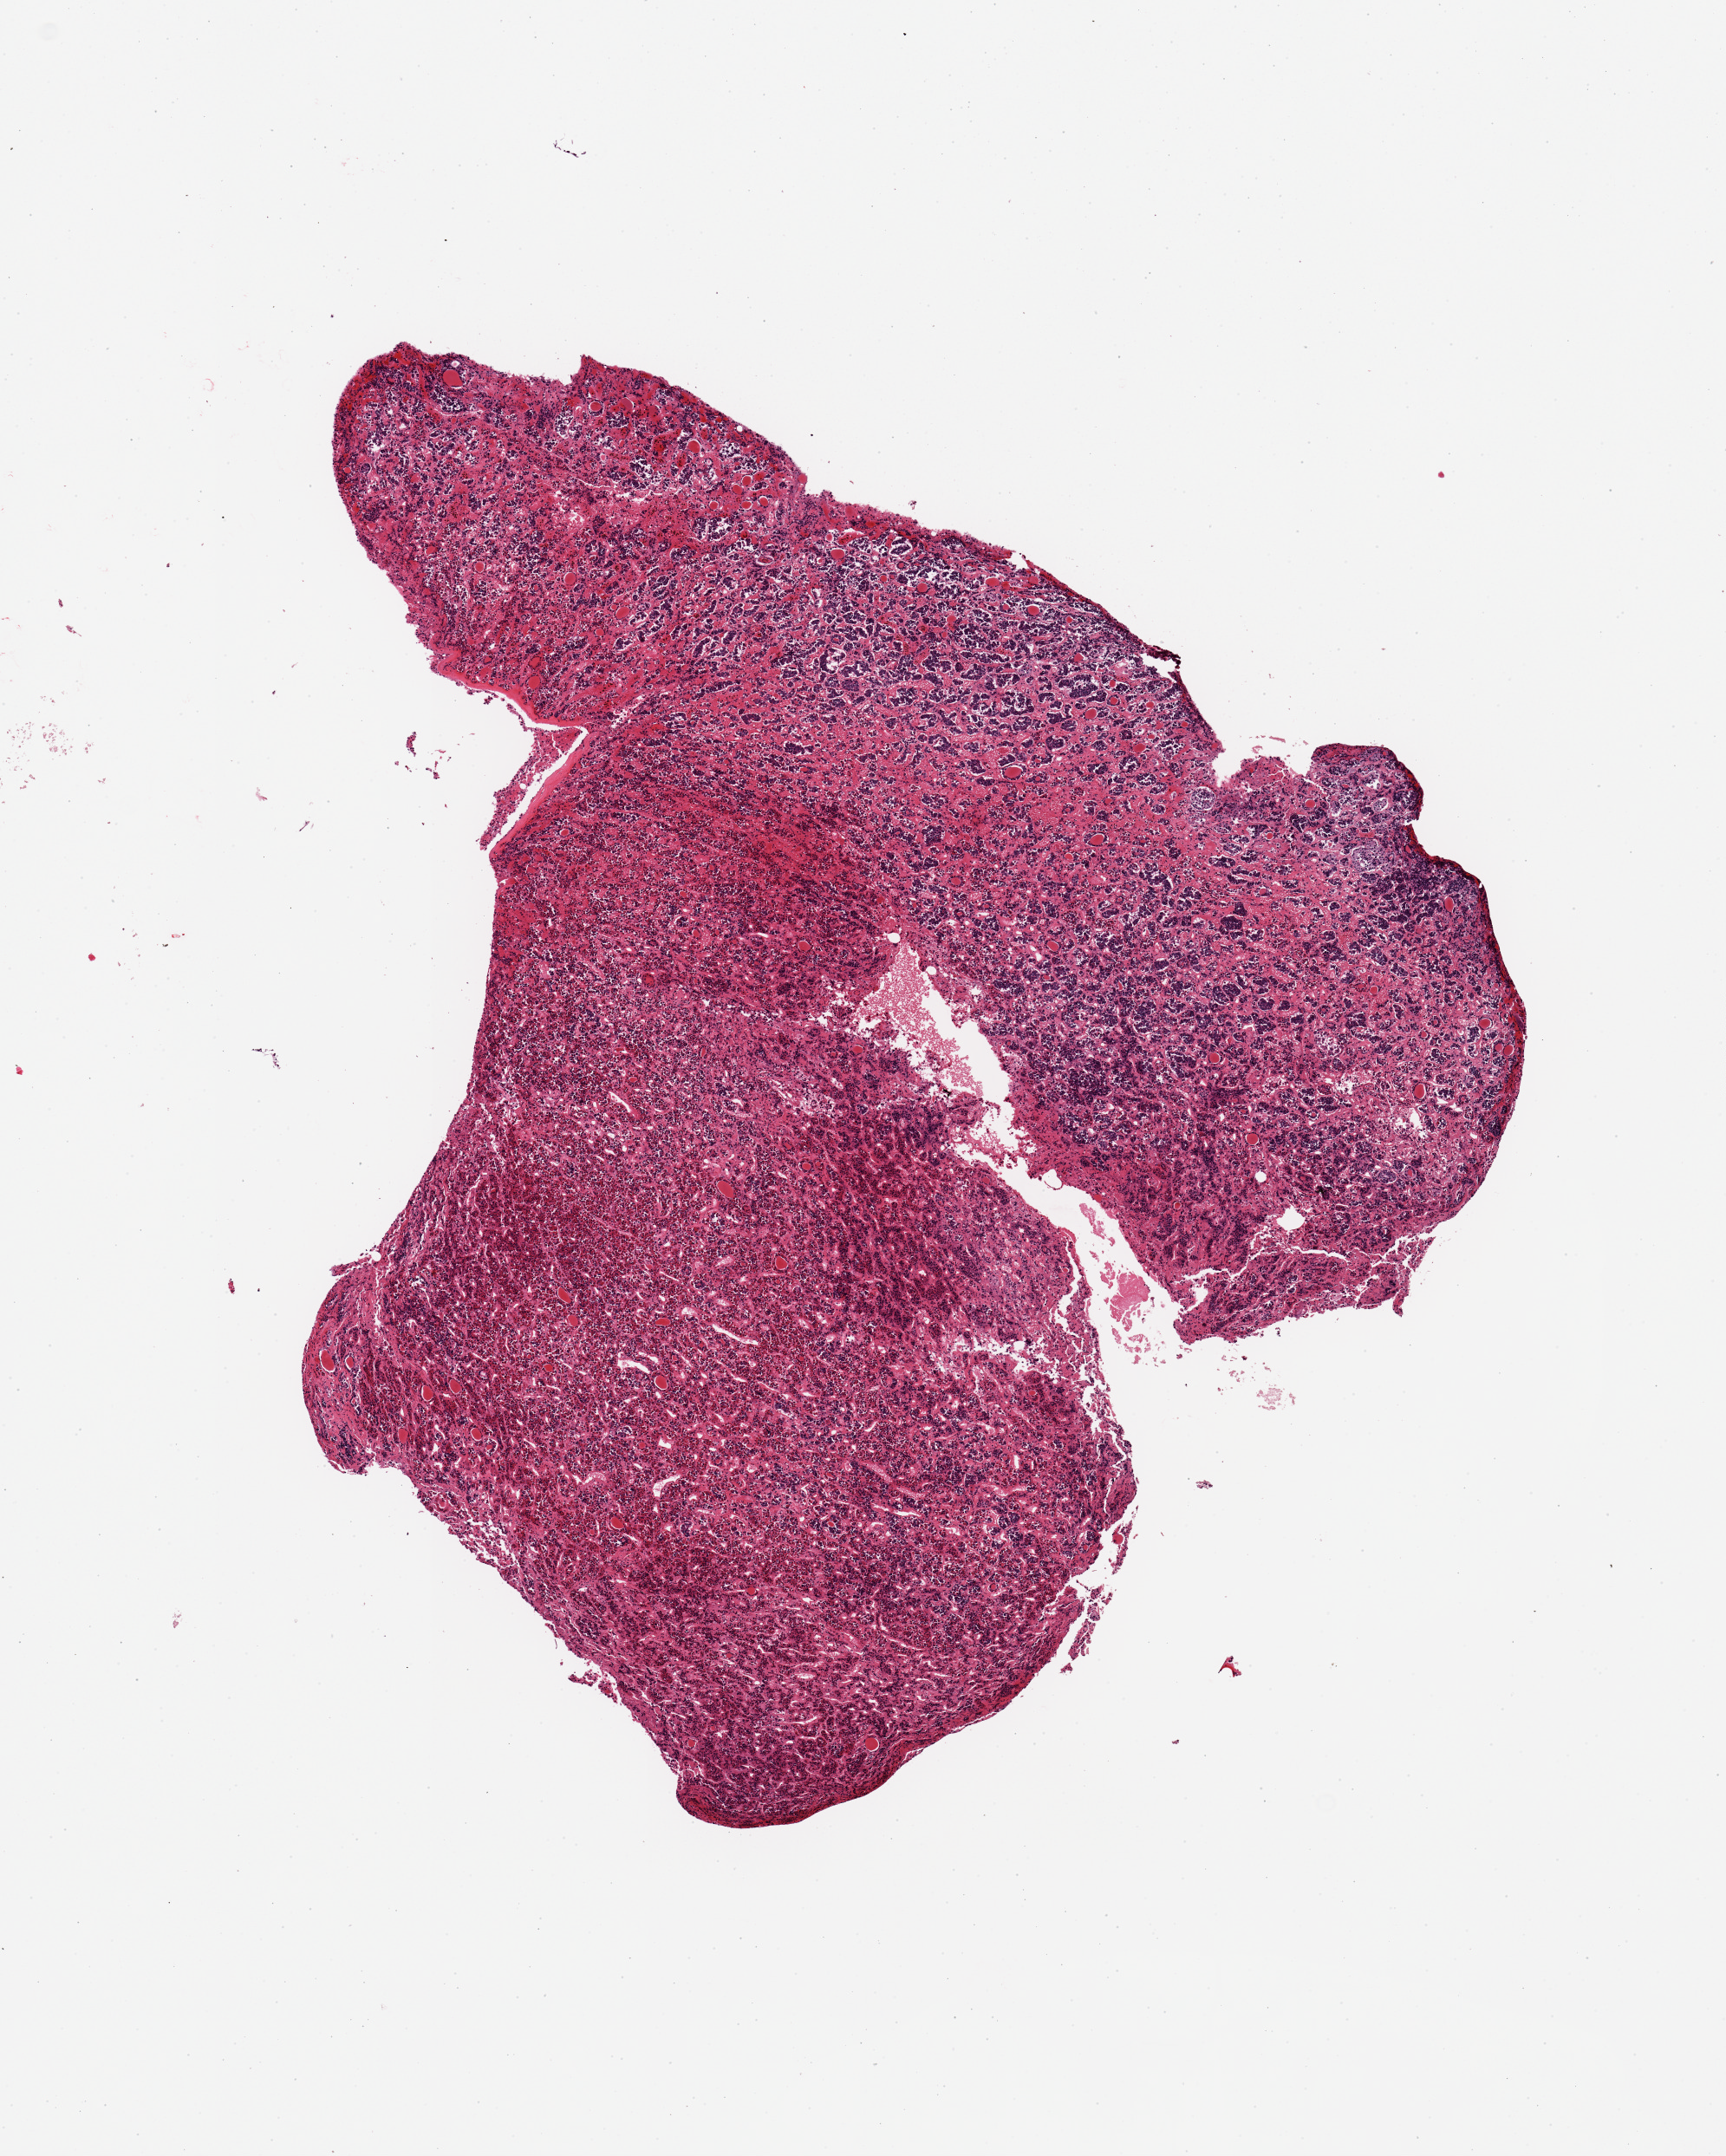
Whole-slide image, haematoxylin and eosin stain, whole scanned area (about 7.9 x 9.8 mm, slide scanned at 20x) shown as a low-resolution overview. PAXgene-fixed, paraffin-embedded tissue. Section of pituitary (target tissue). Donor tissue sample.
• pathologist's review note for this sample: 1 piece; all adenohypophysis